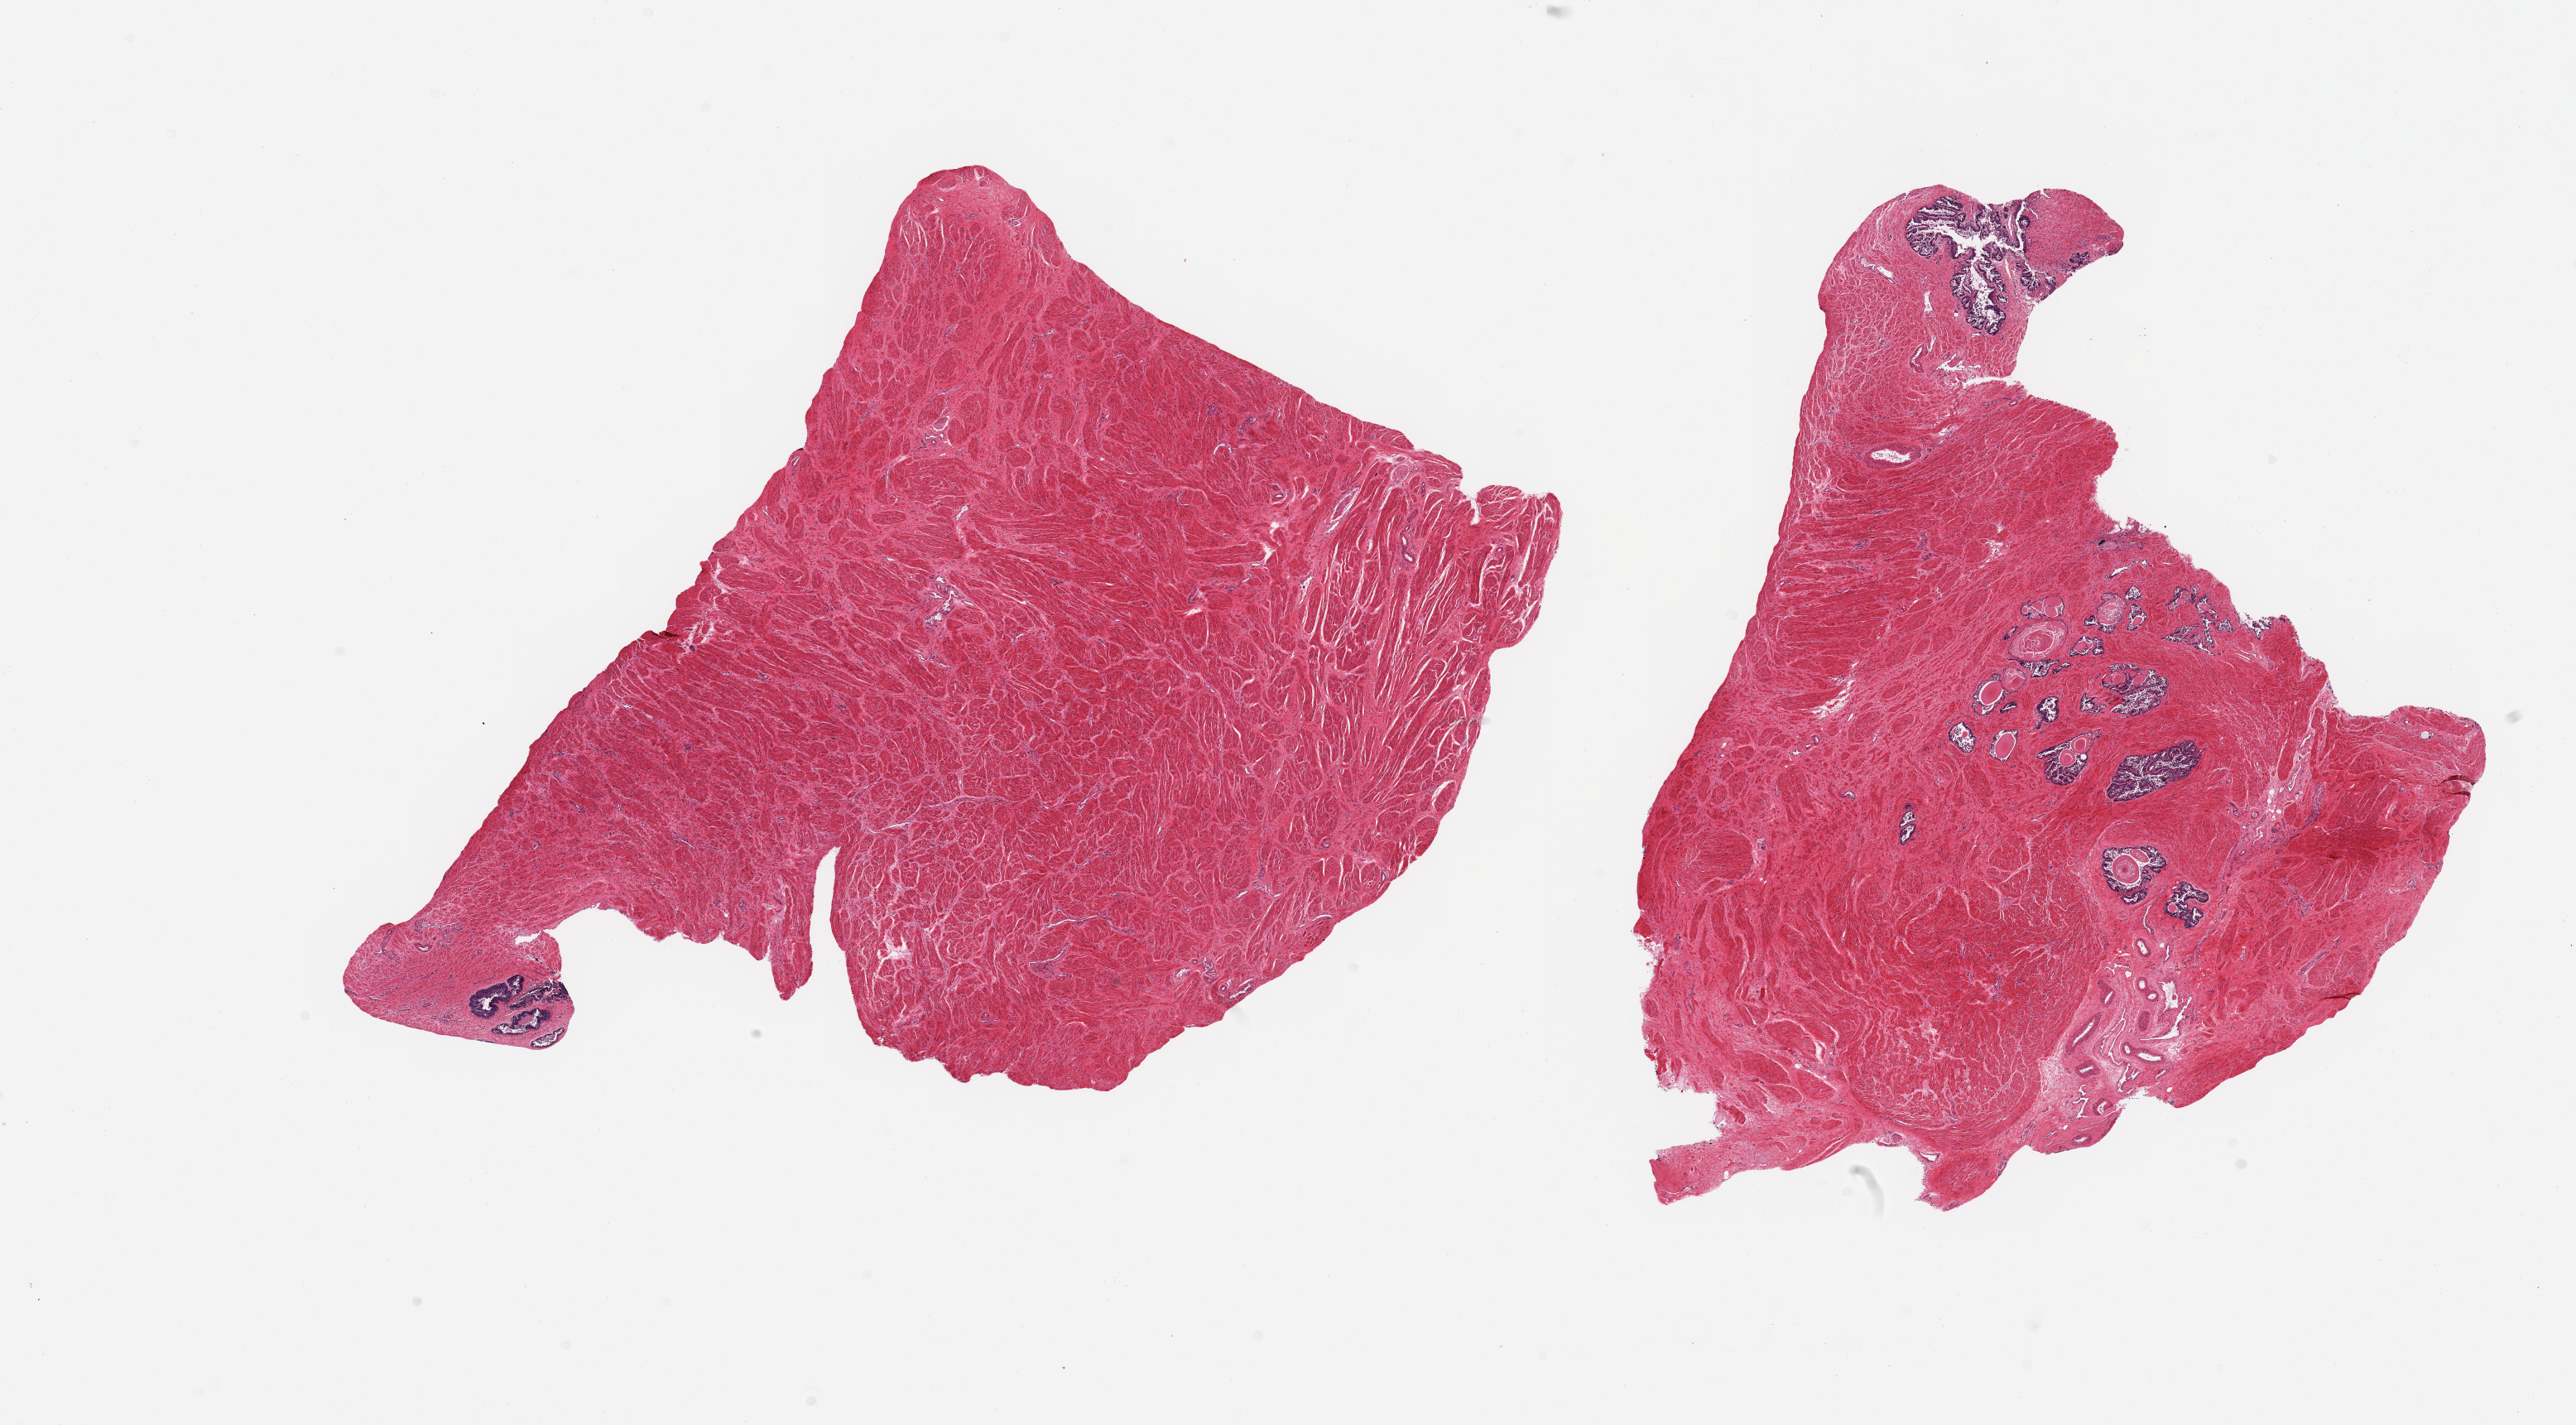
Hematoxylin and eosin (H&E) whole-slide image, brightfield, low-resolution overview of the scanned area, about 24.6 x 13.6 mm (slide scanned at 20x), PAXgene-fixed, paraffin-embedded tissue, section of prostate (target tissue), donor tissue sample. Male donor.
Reviewer comment on this tissue sample: 2 pieces, seminal vesicle/stroma.